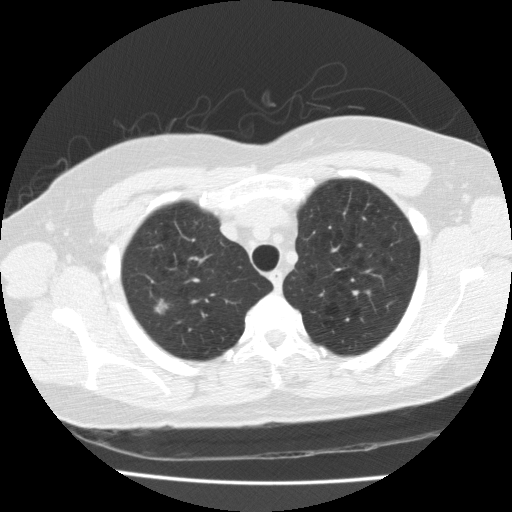
Low-dose screening chest CT, one axial slice; position 146 of 175 along the scan axis; reconstruction kernel FC10; 120 kVp; lung window (W 1500 / L -600 HU); 512 × 512 image matrix.
Outlined on this slice (outlined manually by an expert reader):
- lesion 1 (tumor, upper lobe of right lung): bounding box <155,299,168,314> (left, top, right, bottom; pixels)